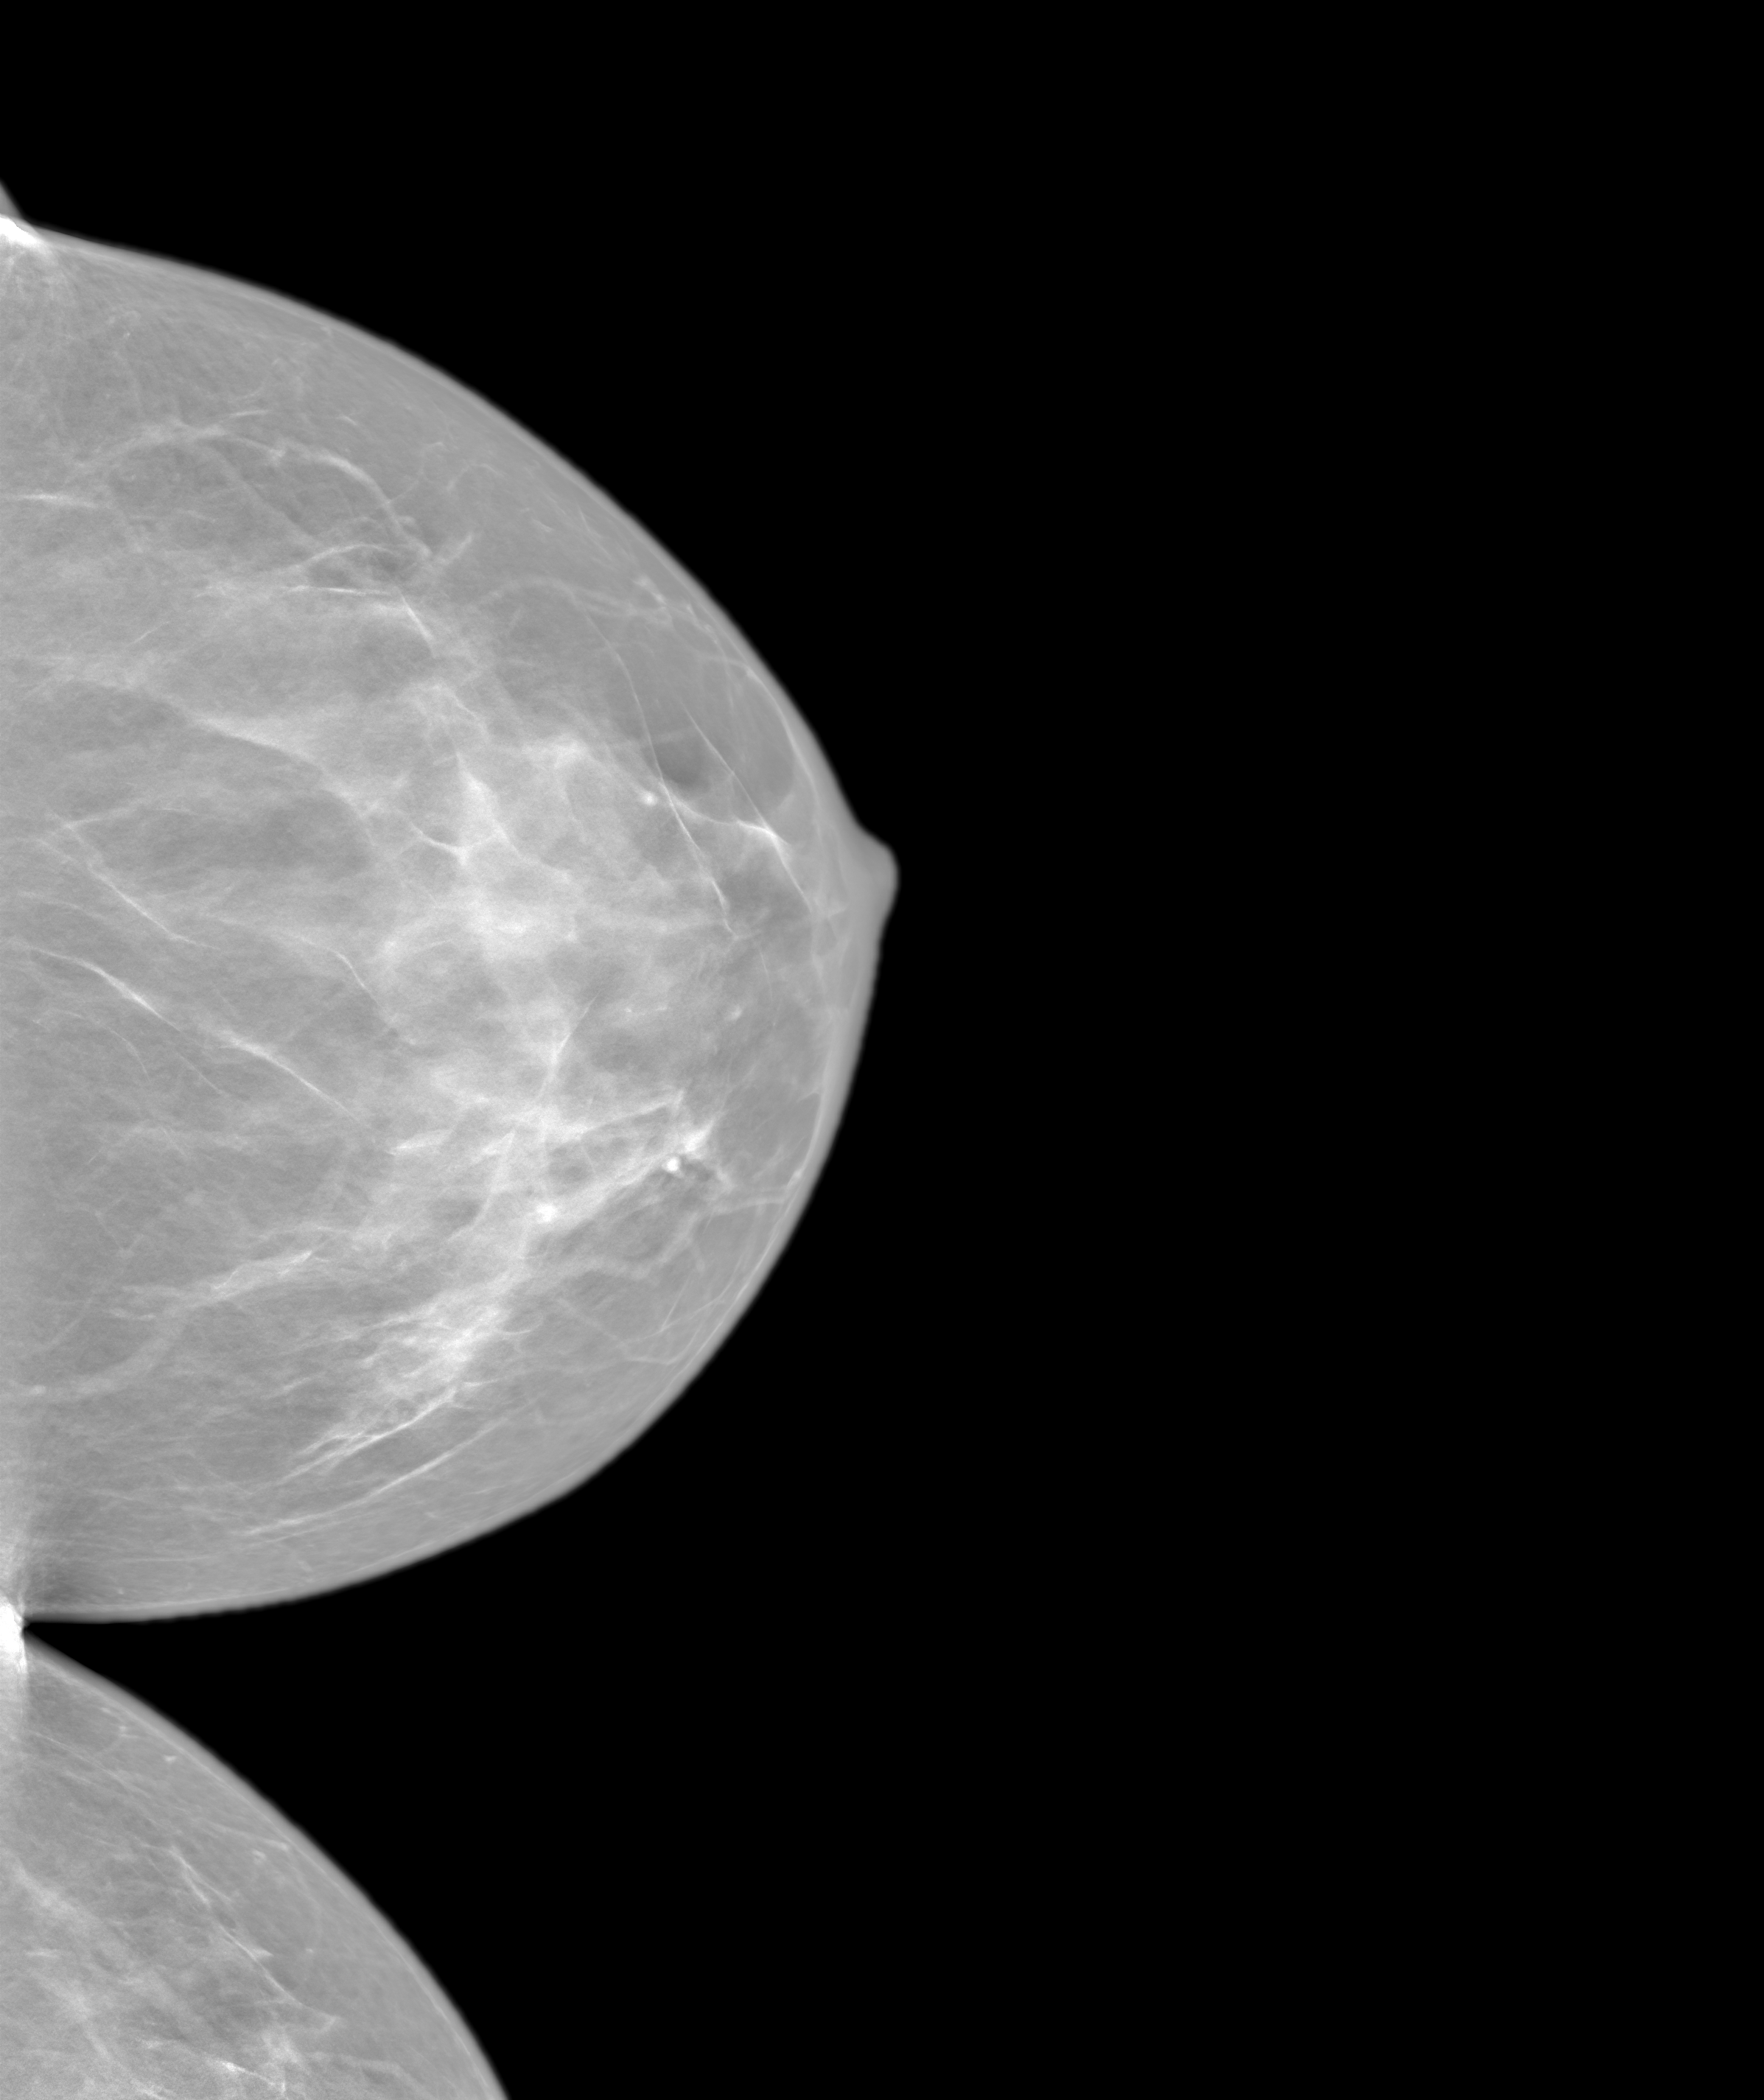
Screening examination. Patient aged 45 years (female).
Image type: synthesized 2-D view from tomosynthesis. Breast: left. Projection: craniocaudal (CC) view.